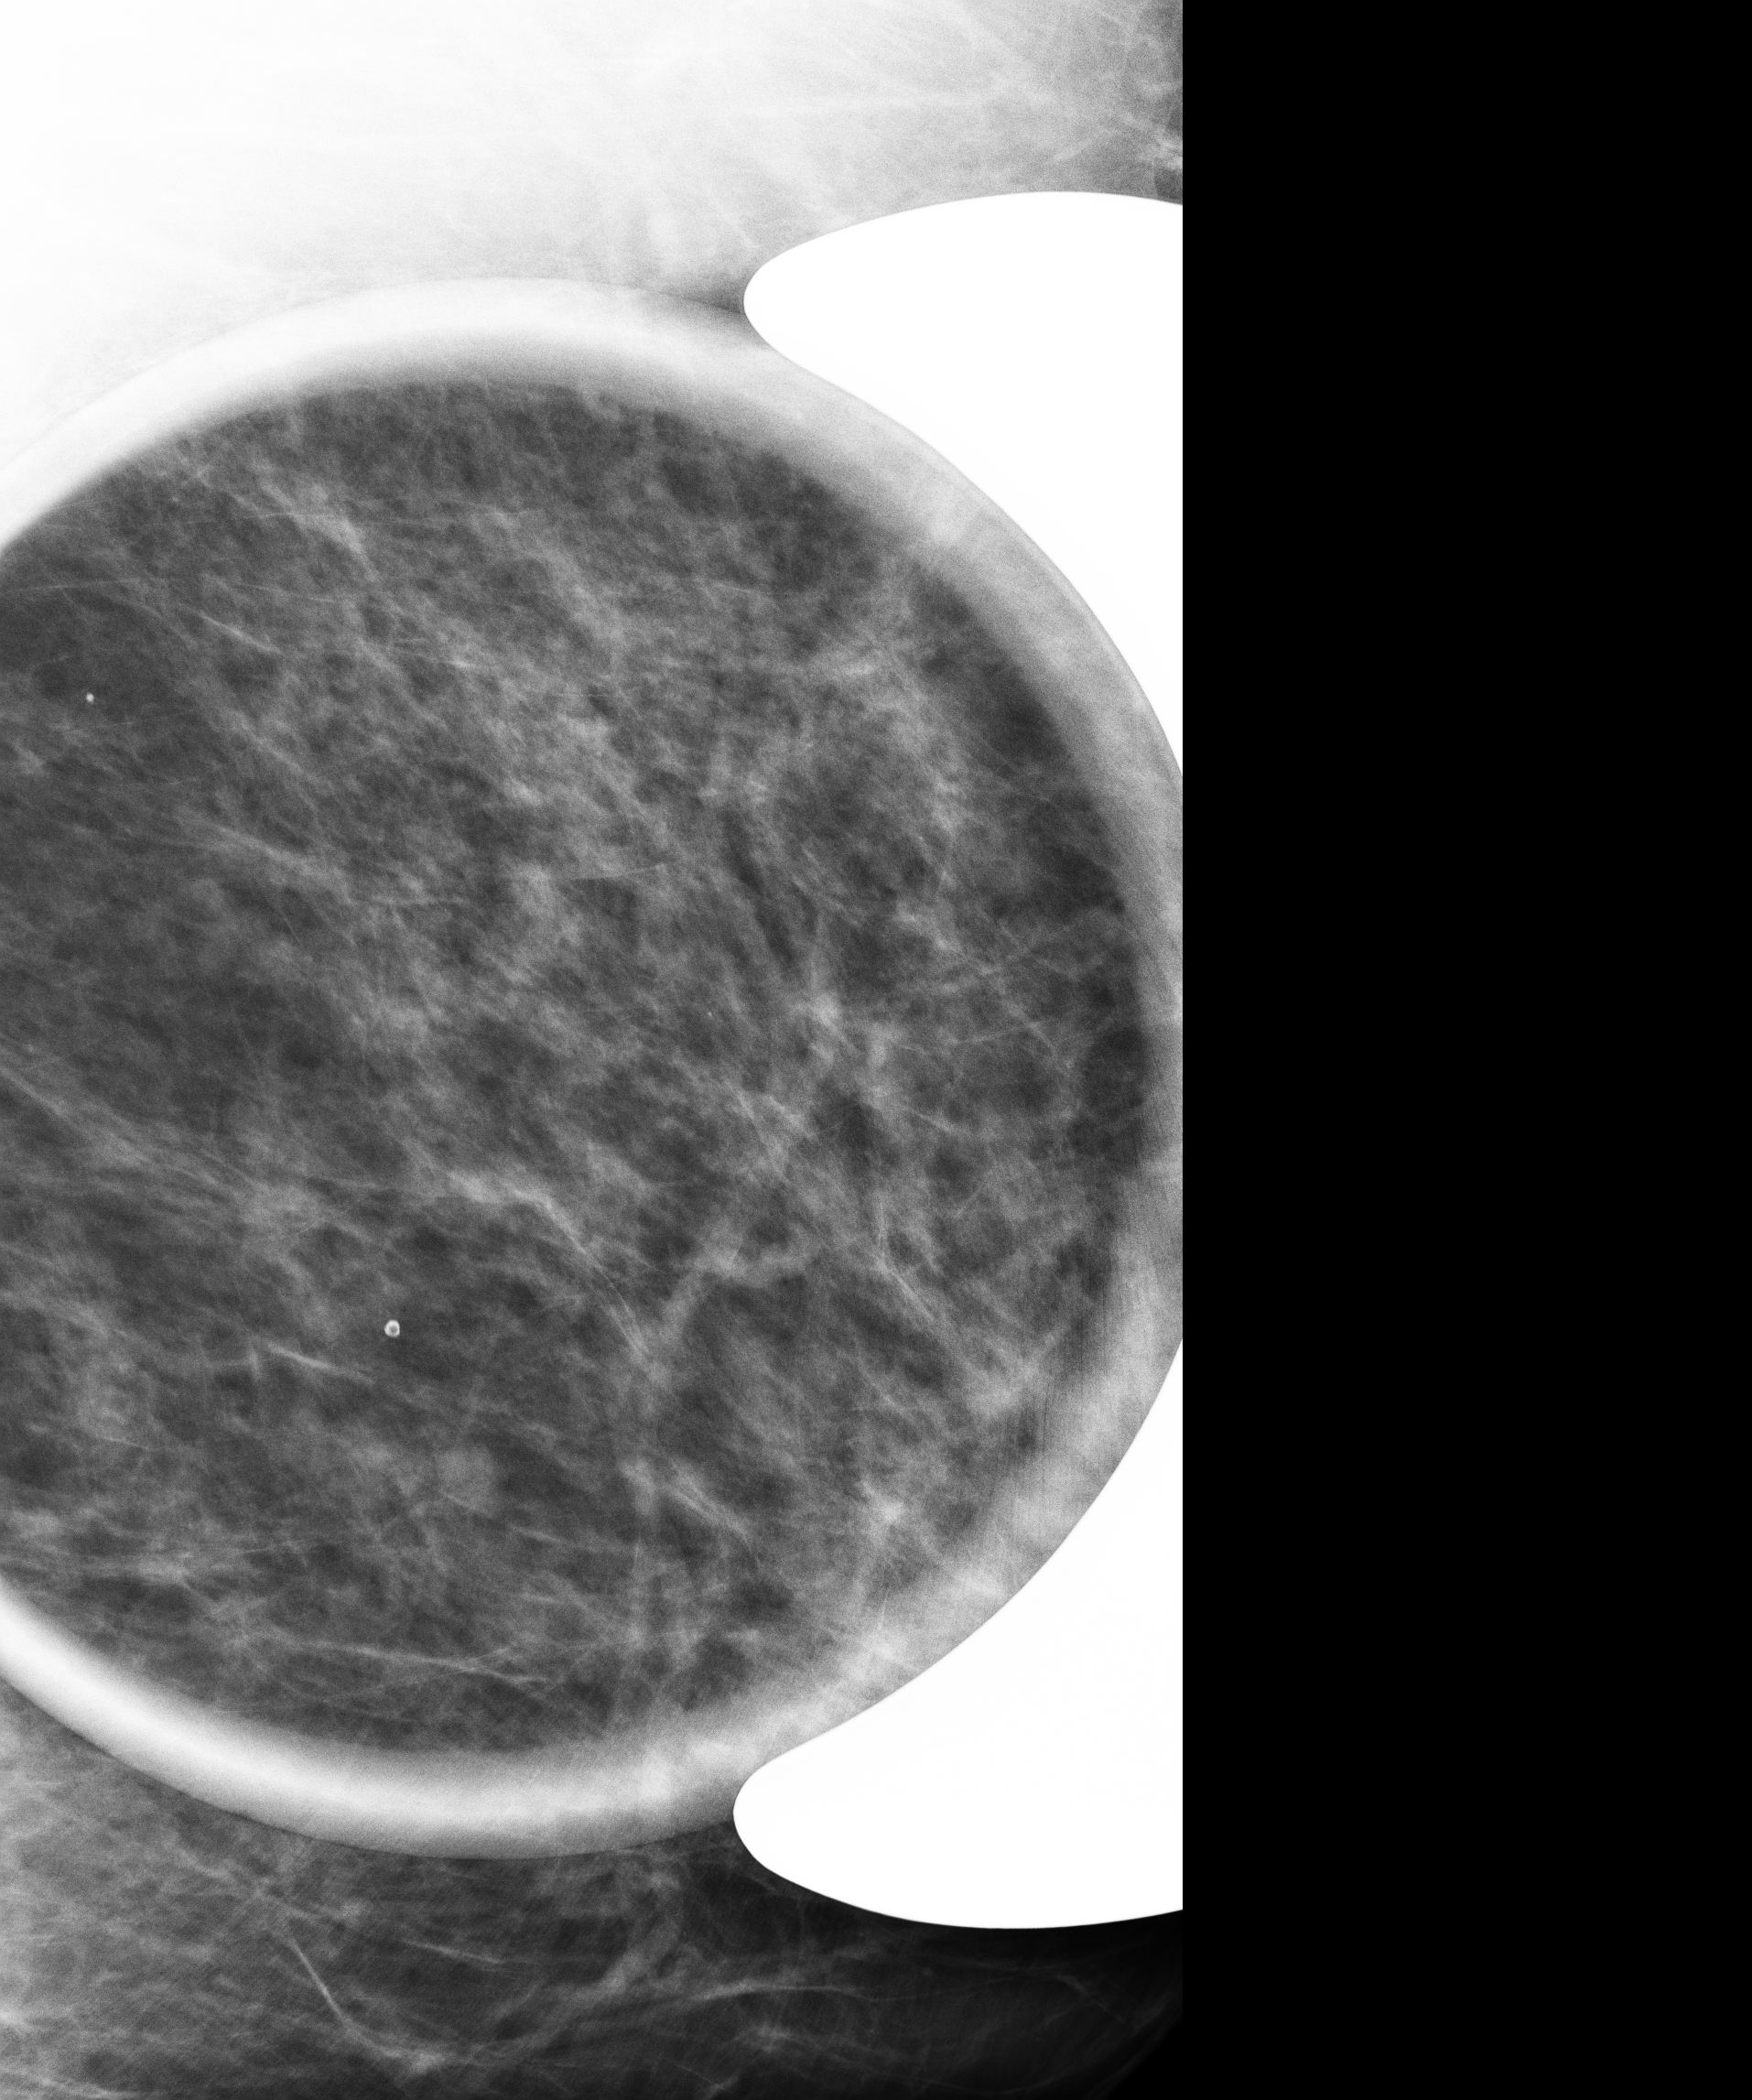
Full-field digital mammogram (FFDM), left breast, mediolateral (ML) view, diagnostic examination (additional views), compressed breast thickness 74 mm. Female patient, age 53 years.
Breast density at the screening exam (both breasts): heterogeneously dense (BI-RADS density category c). Final BI-RADS category for the screening round (tomosynthesis exam, both breasts): category 4. Recall: recalled for additional imaging after this screen.